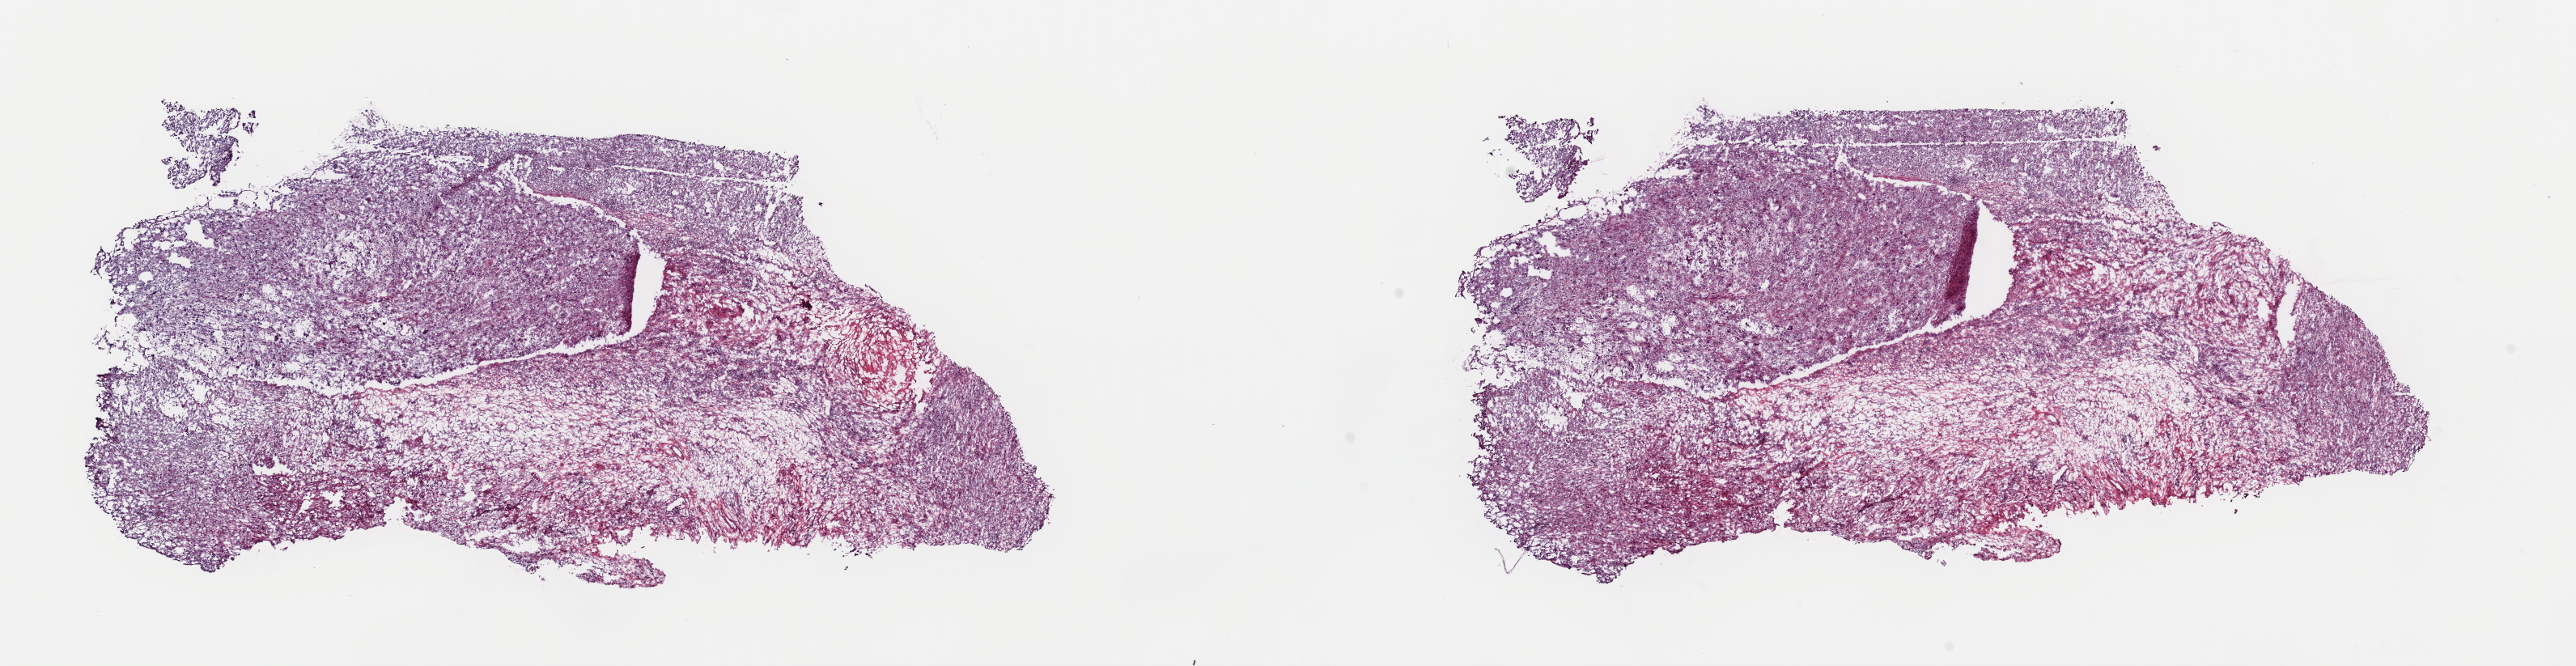
Whole-slide histology image, H&E-stained — shown as a low-resolution overview of the whole scanned area (about 25.1 x 6.5 mm); frozen section from the top of the tissue portion; sample: primary tumour, connective, subcutaneous and other soft tissues. Patient sex: male. Slide review estimates, as recorded: tumour cells 85%, tumour nuclei 100%, normal cells 0%, stromal cells 15%, necrosis 0%. Inflammatory infiltration, as recorded: lymphocyte infiltration 2%, monocyte infiltration 0%, neutrophil infiltration 0%.
Histologic diagnosis: Undifferentiated sarcoma (connective, subcutaneous and other soft tissues of lower limb and hip).